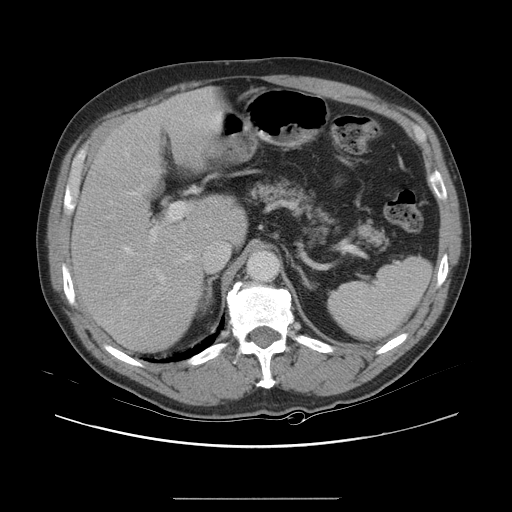
Contrast-enhanced abdominal CT, one axial slice; slice 16 of 40 in the series (ordered by position); 120 kVp; intravenous contrast given; soft-tissue window (W 400 / L 40 HU); 5 mm slice thickness; 512 × 512 image matrix, field of view 408 × 408 mm. Male patient, age 64 years. Case-level facts recorded for this patient, not image findings: diagnosis: colorectal cancer liver metastases, imaged before liver resection; multiple liver metastases: yes; largest metastasis: 3.2 cm; chemotherapy before resection: yes.
Annotated regions visible in this slice (manually delineated by an expert):
- hepatic veins: bounding box <124,186,144,303> (left, top, right, bottom; pixels)
- liver: <73,91,246,350>
- planned liver remnant (the part of the liver to remain after resection): <88,90,246,244>
- portal vein (with intrahepatic branches): <152,203,185,280>